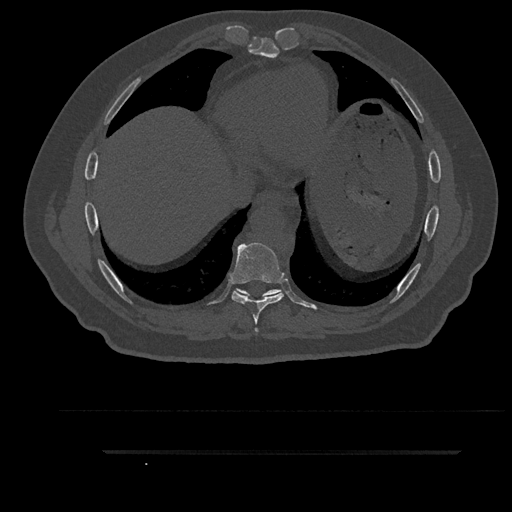
CT including the spine, one axial slice. Position 462 of 797 along the scan axis. Bone window (W 1800 / L 400 HU). 0.5 mm slice thickness. 512 × 512 image matrix, field of view 432 × 432 mm. Patient: male, 63 years. From the clinical record (not read from this slice): primary cancer: renal.
Structures marked on this image (semi-automatically segmented with operator editing):
- T7 vertebra: bounding box (x1, y1, x2, y2) in pixels: (255, 328, 258, 332)
- T8 vertebra: (231, 242, 284, 324)
- T9 vertebra: (235, 289, 282, 299)